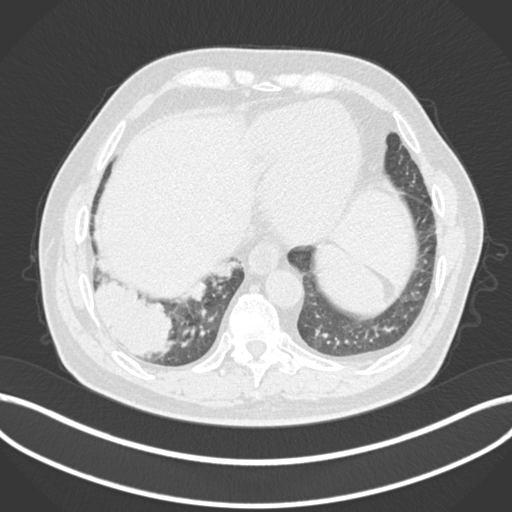
Chest CT, one axial slice. Position 28 of 200 along the scan axis. Reconstruction kernel B30f. 120 kVp. Lung window (W 1500 / L -600 HU). 1 mm slice thickness. 512 × 512 image matrix, field of view 400 × 400 mm. Male patient, age 59 years.
Outlined on this slice (rectangle marked by the reading radiologist):
- lung tumour (recorded histology: adenocarcinoma): bounding box <93,275,173,360> (left, top, right, bottom; pixels)